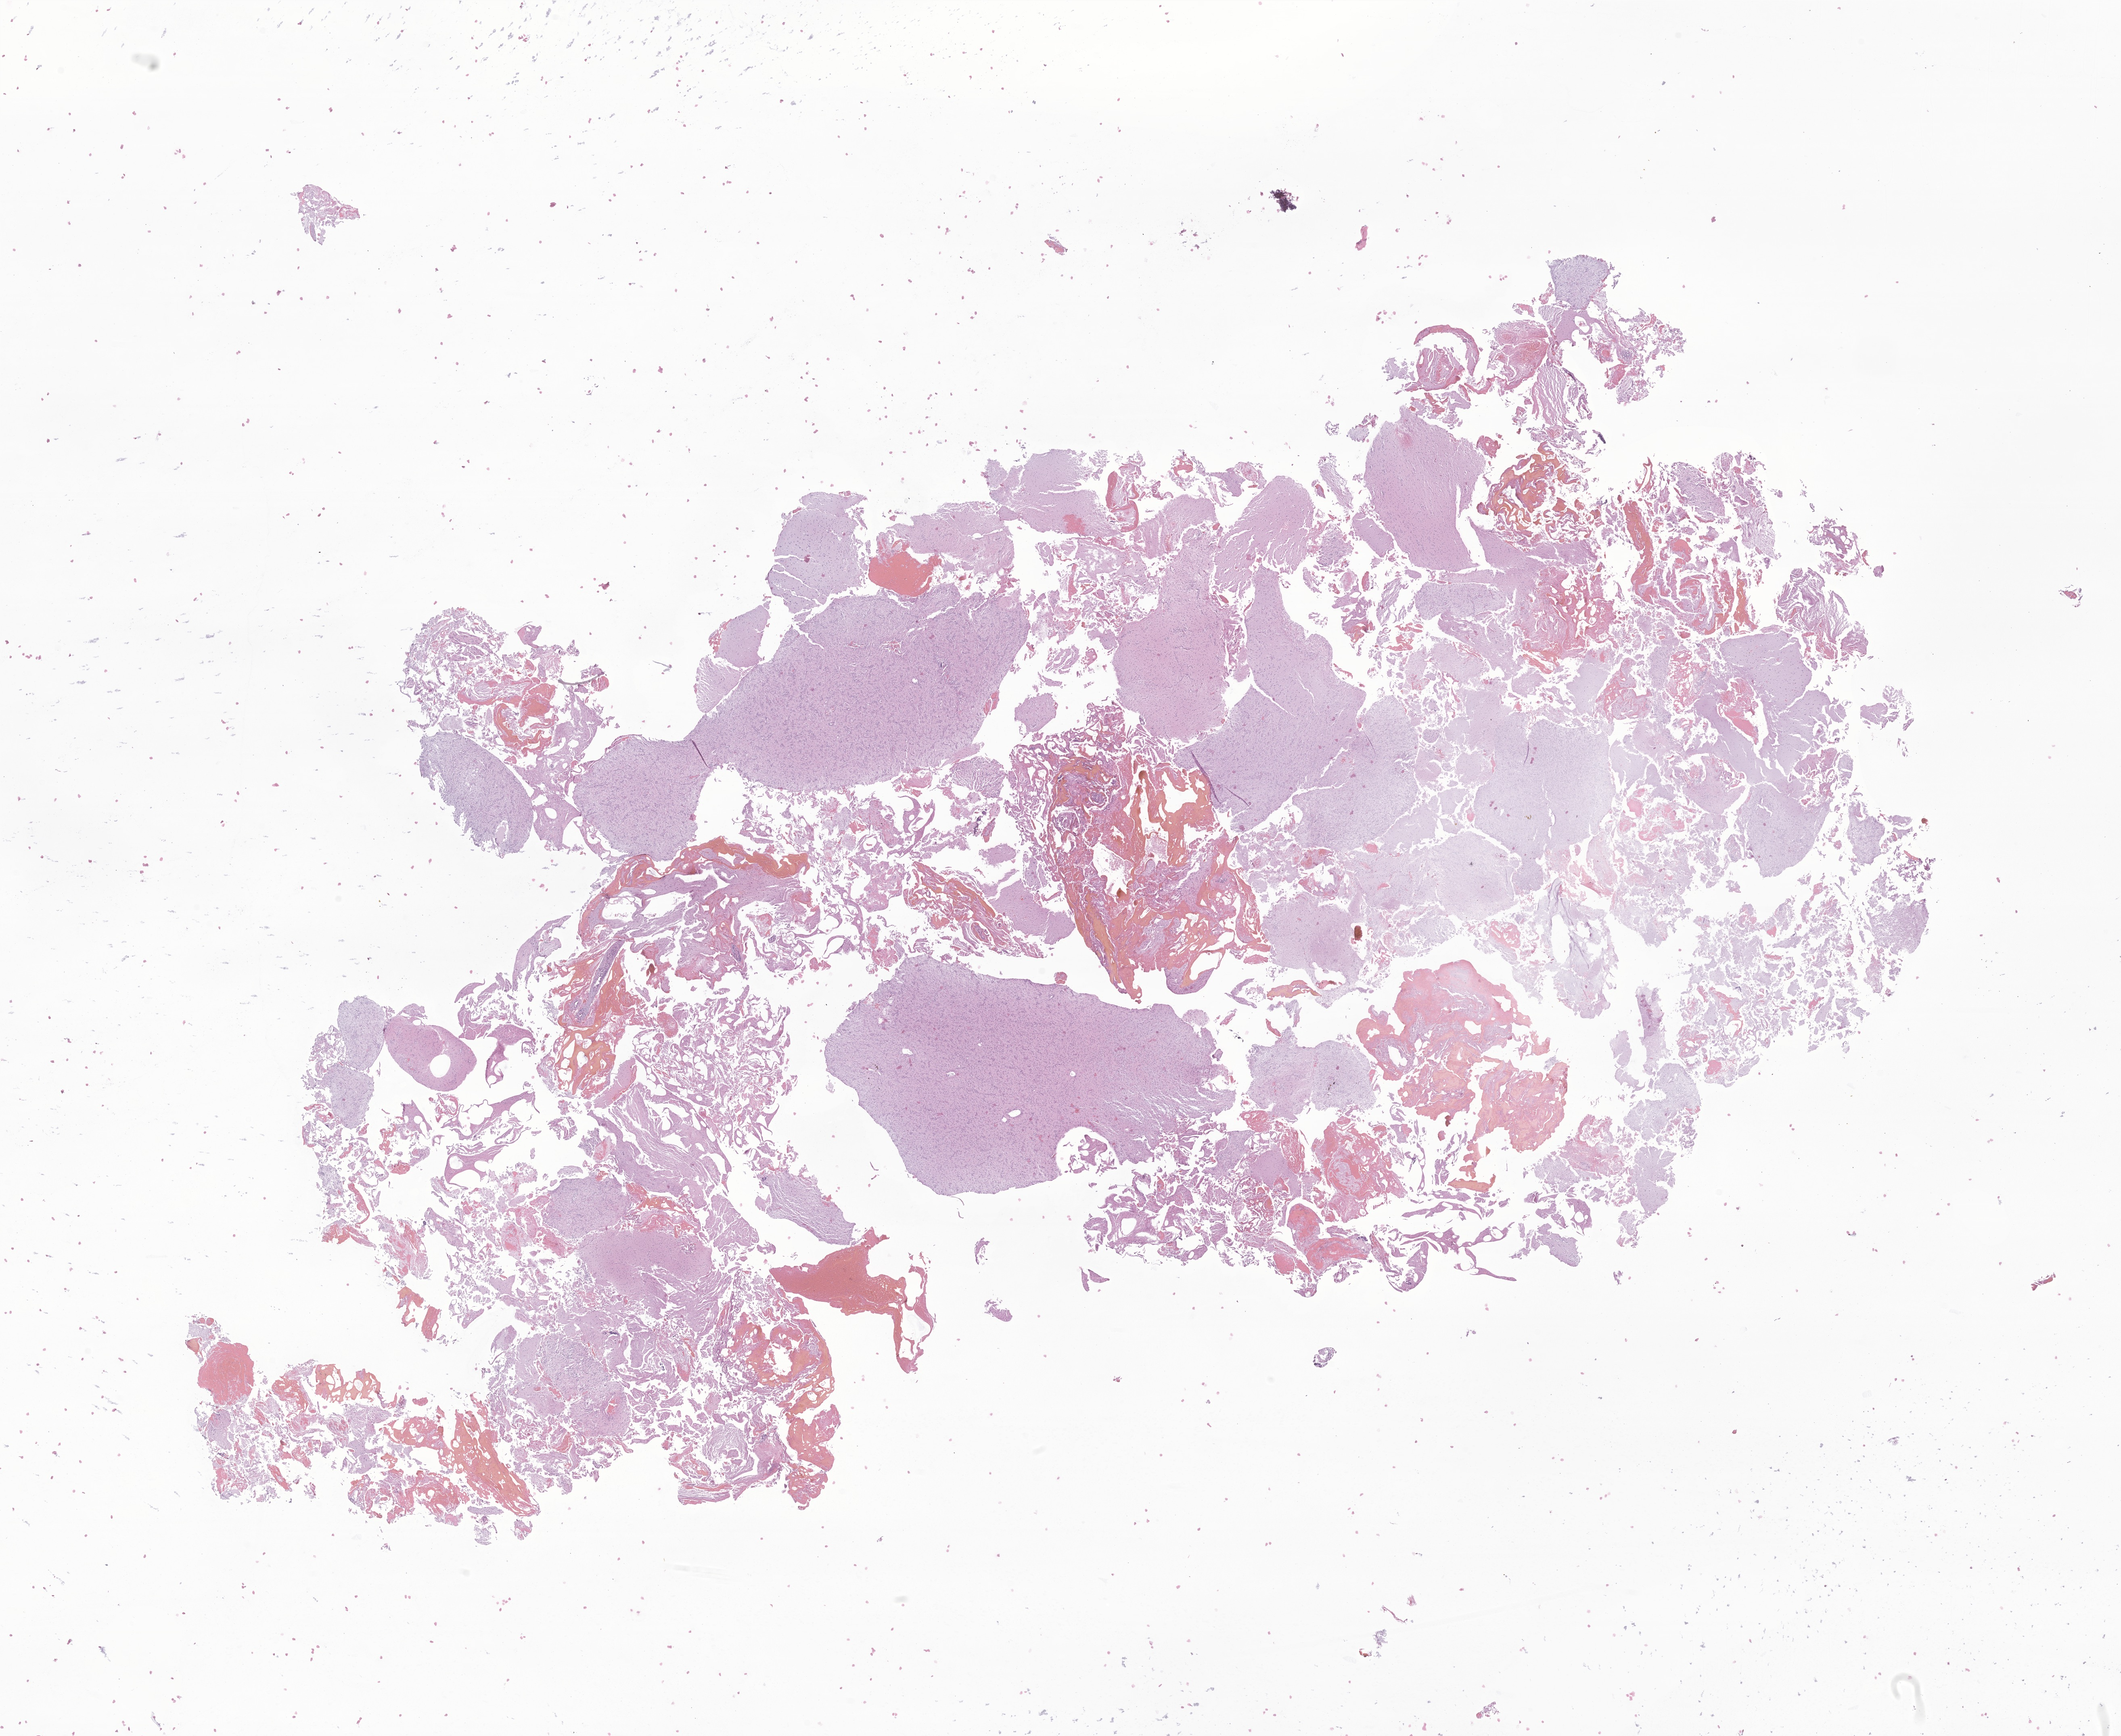
Digitized H&E-stained section of tumor tissue from the cerebral ventricle — a low-resolution overview of the entire scanned area, about 22.2 x 18.1 mm; FFPE section. Female patient, age 100 months.
Diagnosis (ICD-O-3 morphology term): Glioma, malignant.